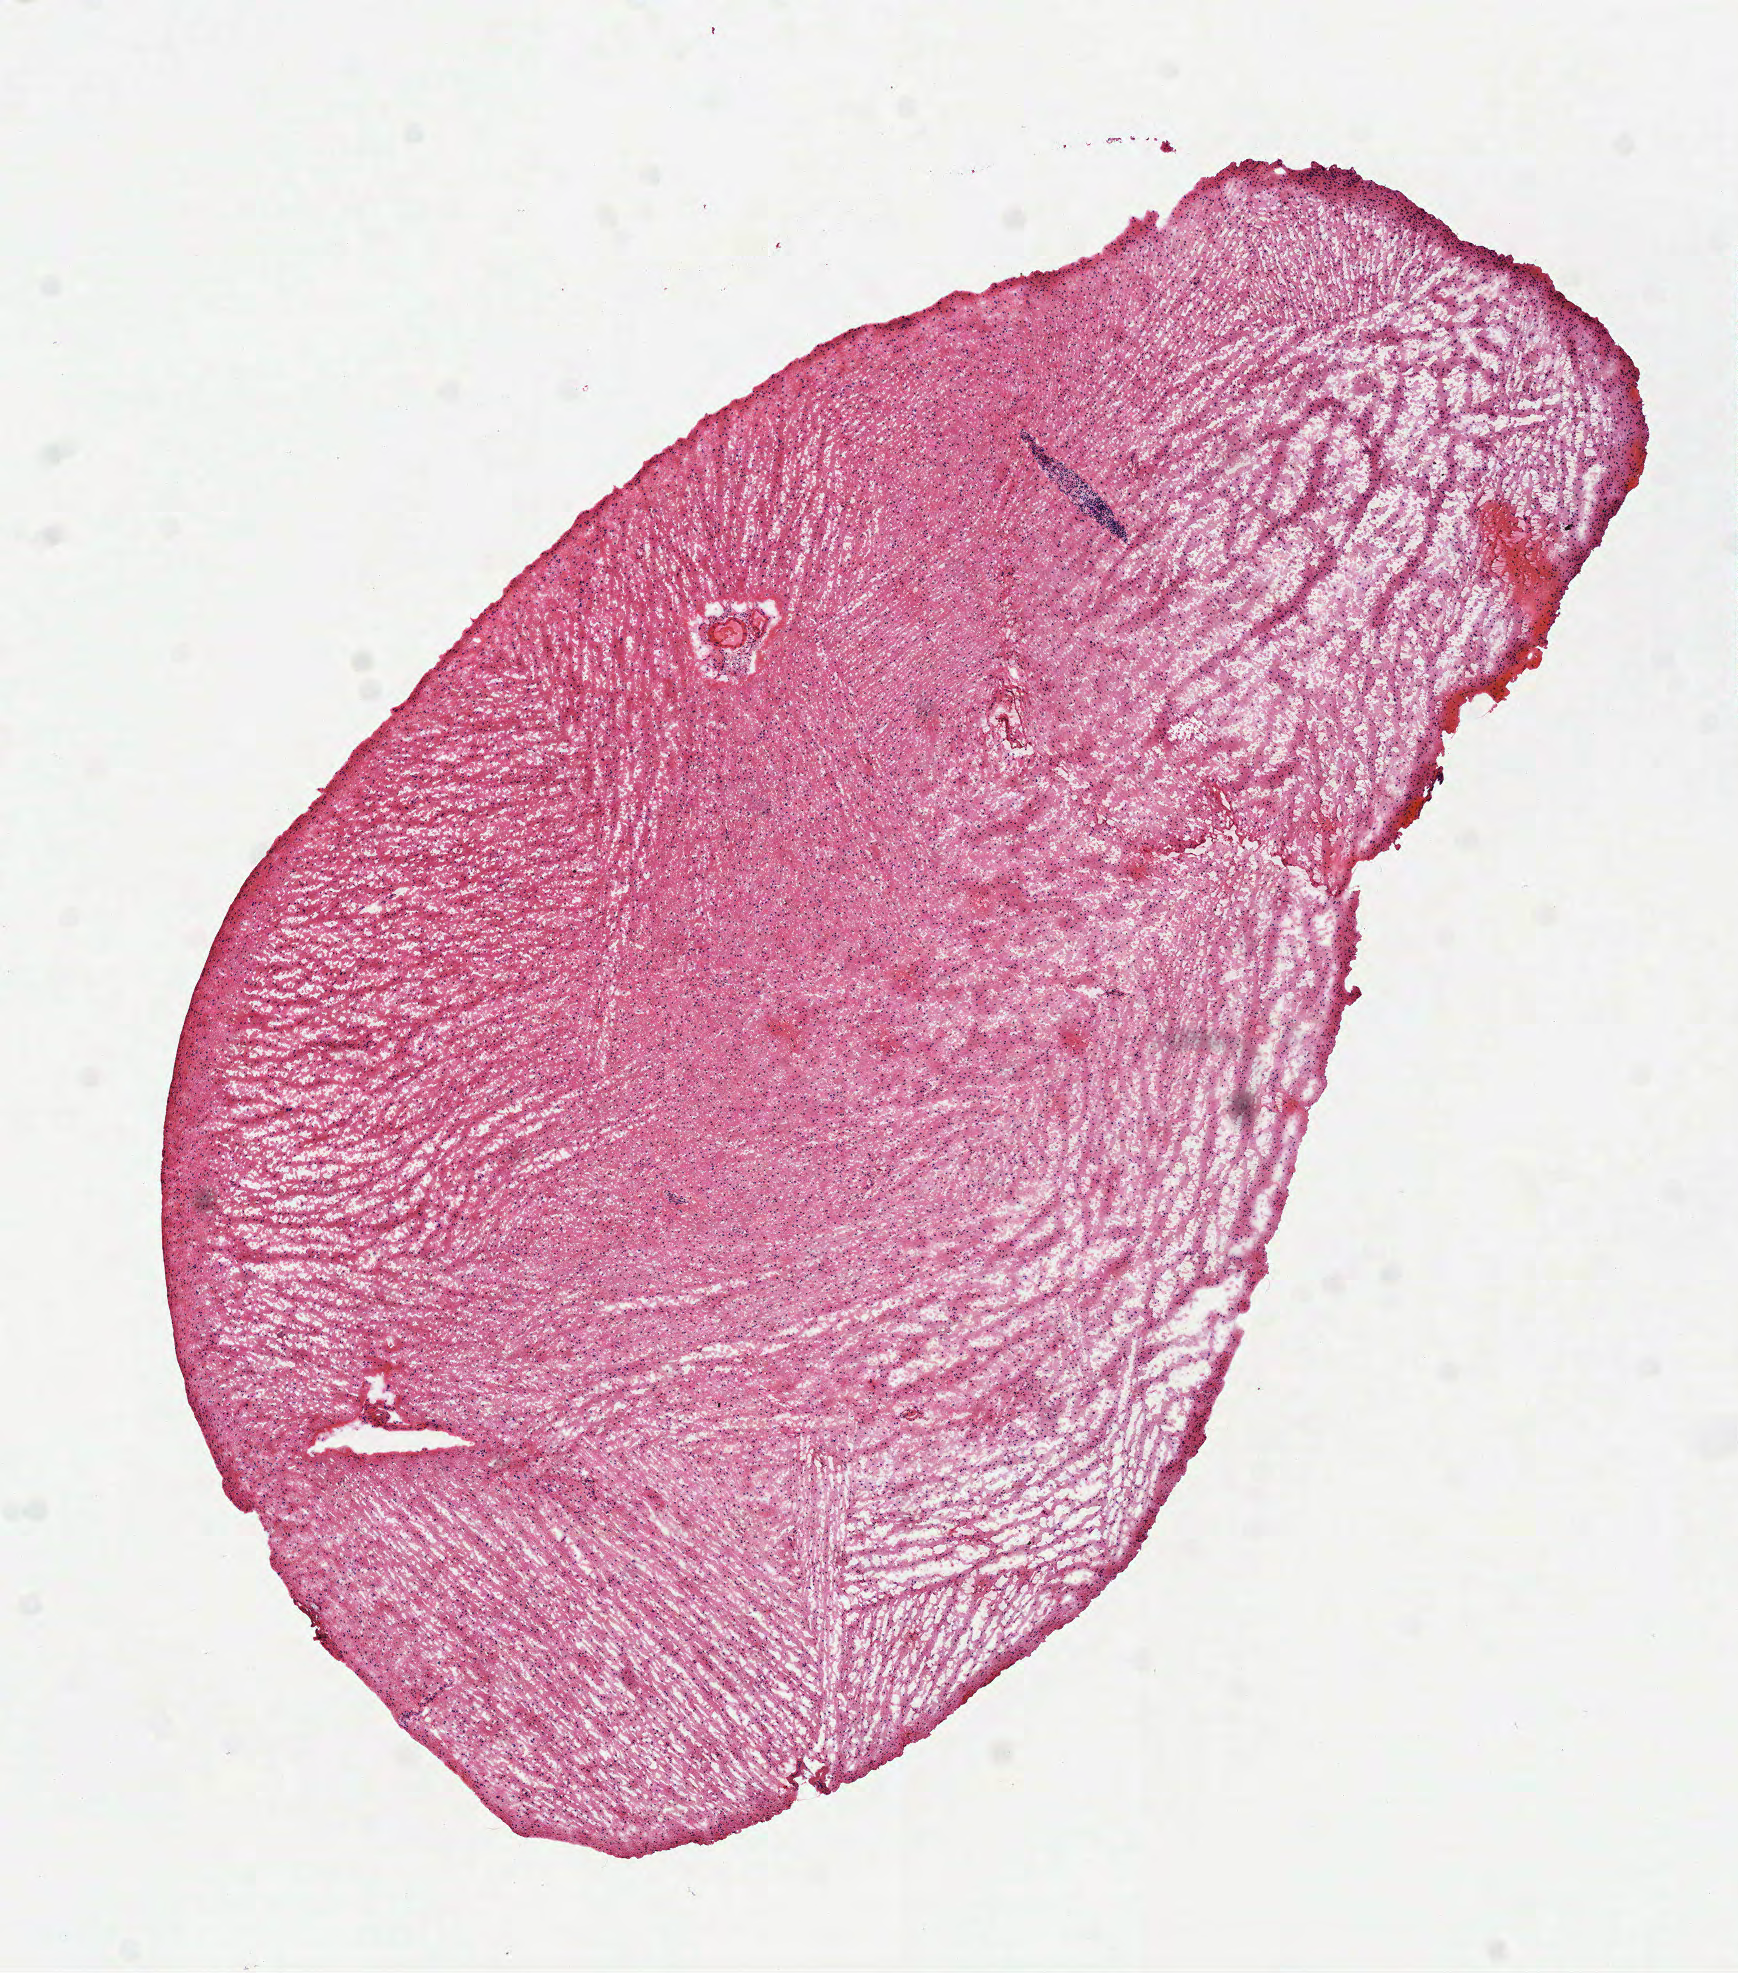
Hematoxylin and eosin (H&E) stained whole-slide image, low-resolution overview of the scanned area, about 7.0 x 8.0 mm; frozen section from the top of the tissue portion; primary tumour sample from the brain. Male patient; age at initial diagnosis 31 years. Histologic grade: G3 (poorly differentiated). Pathologist review of this section (percent, as recorded): tumour cells 100%, tumour nuclei 65%, normal cells 0%, stromal cells 0%, necrosis 0%.
Histologic diagnosis: Astrocytoma, anaplastic.